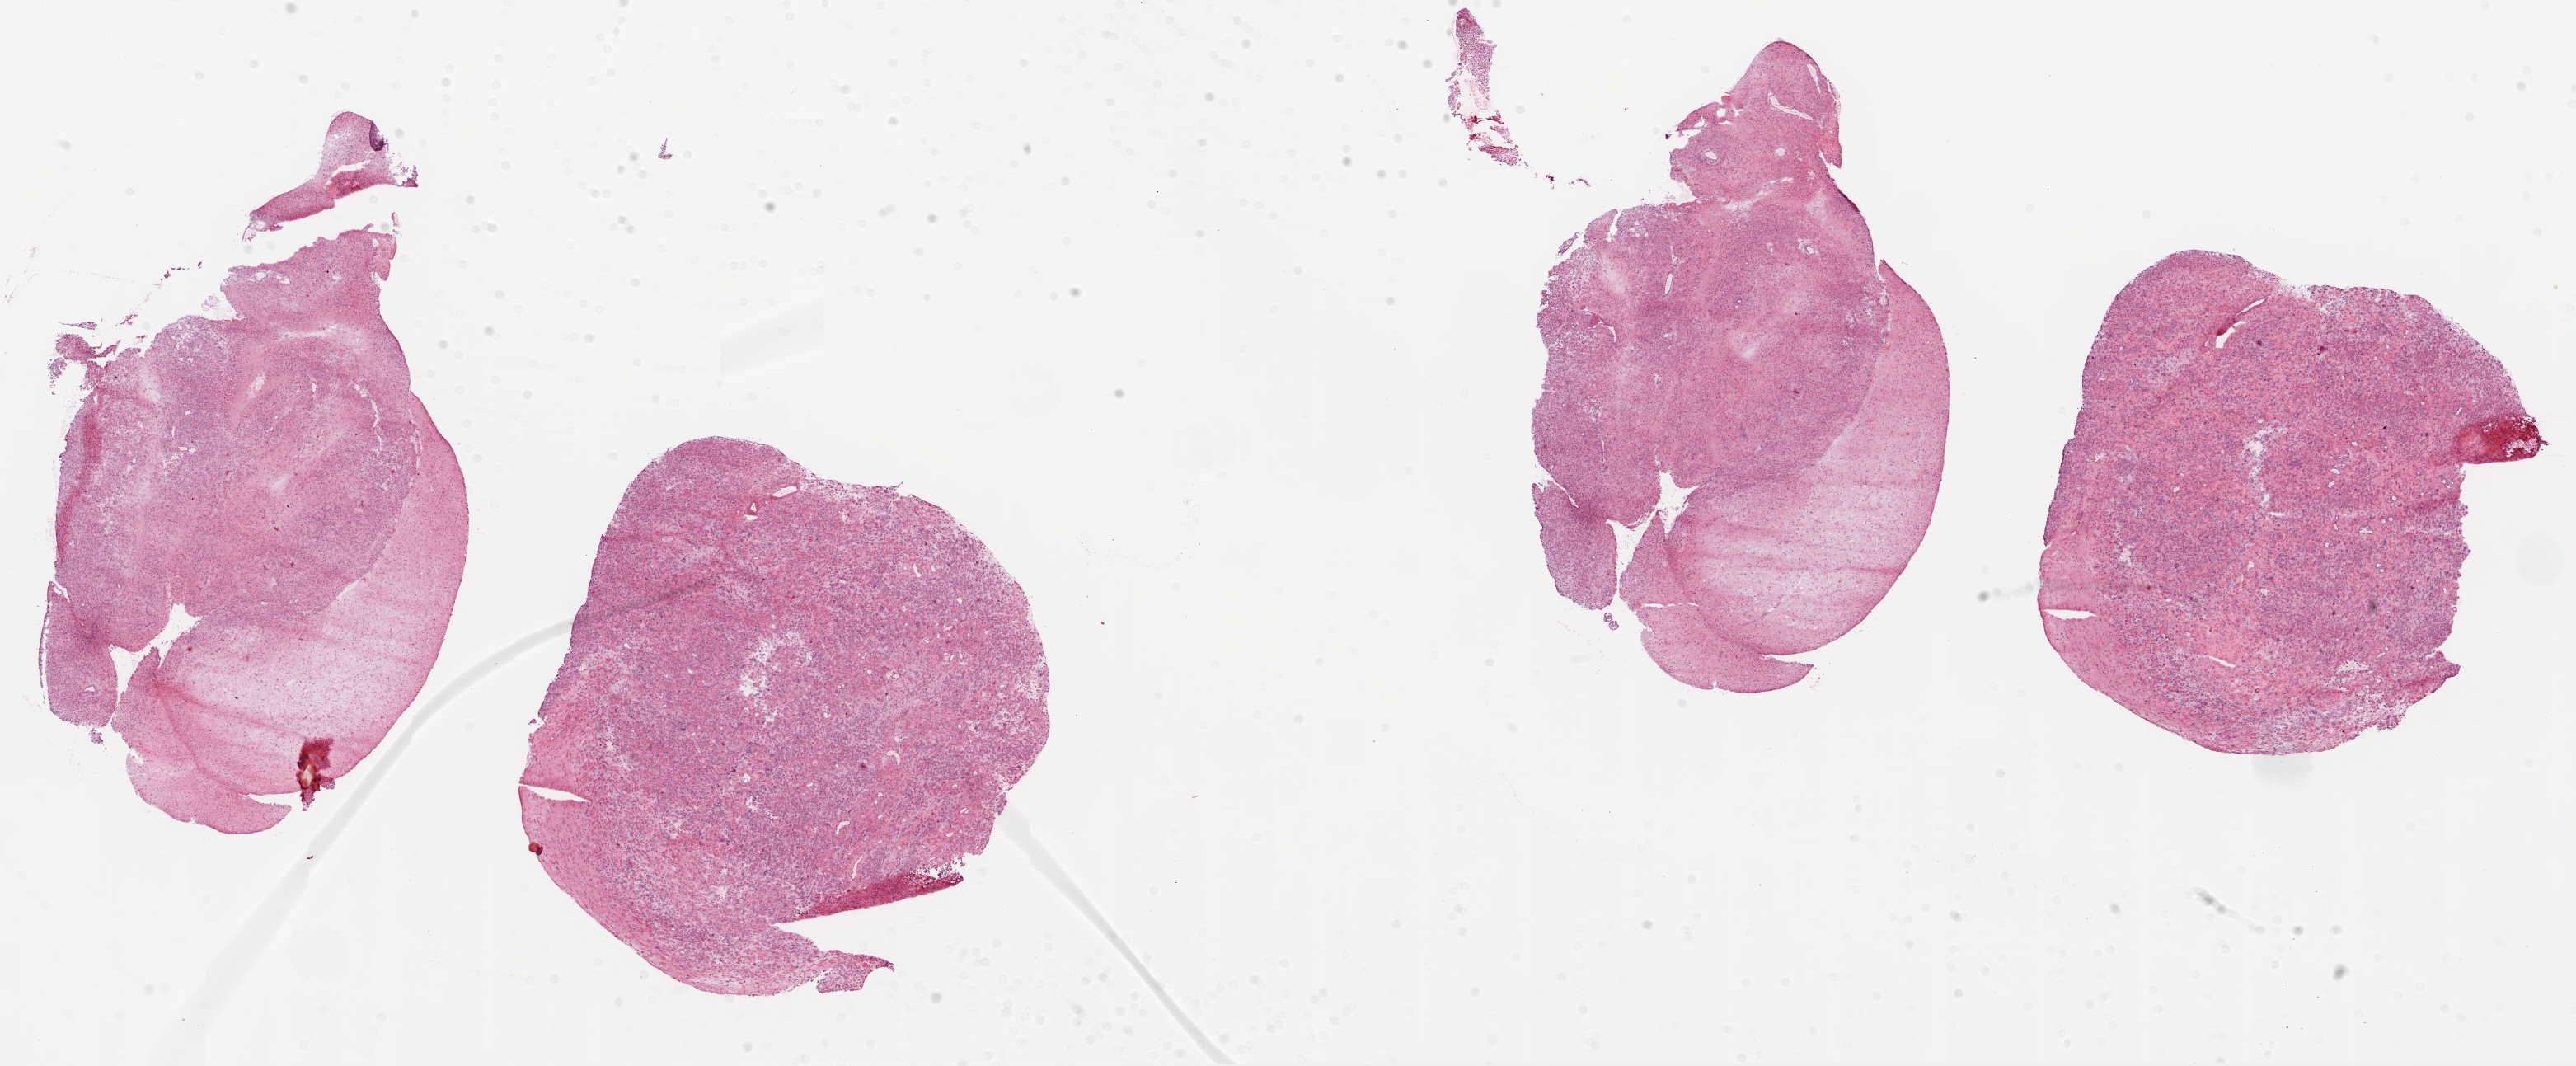
H&E whole-slide image, a low-resolution overview of the entire scanned area, about 25.1 x 10.4 mm (from a 20x scan); frozen section; primary tumour sample from the brain. Male, age 34 years at initial diagnosis. Slide review estimates, as recorded: tumour cells 95%, tumour nuclei 85%, normal cells 0%, stromal cells 0%, necrosis 5%.
Histologic diagnosis: Glioblastoma.